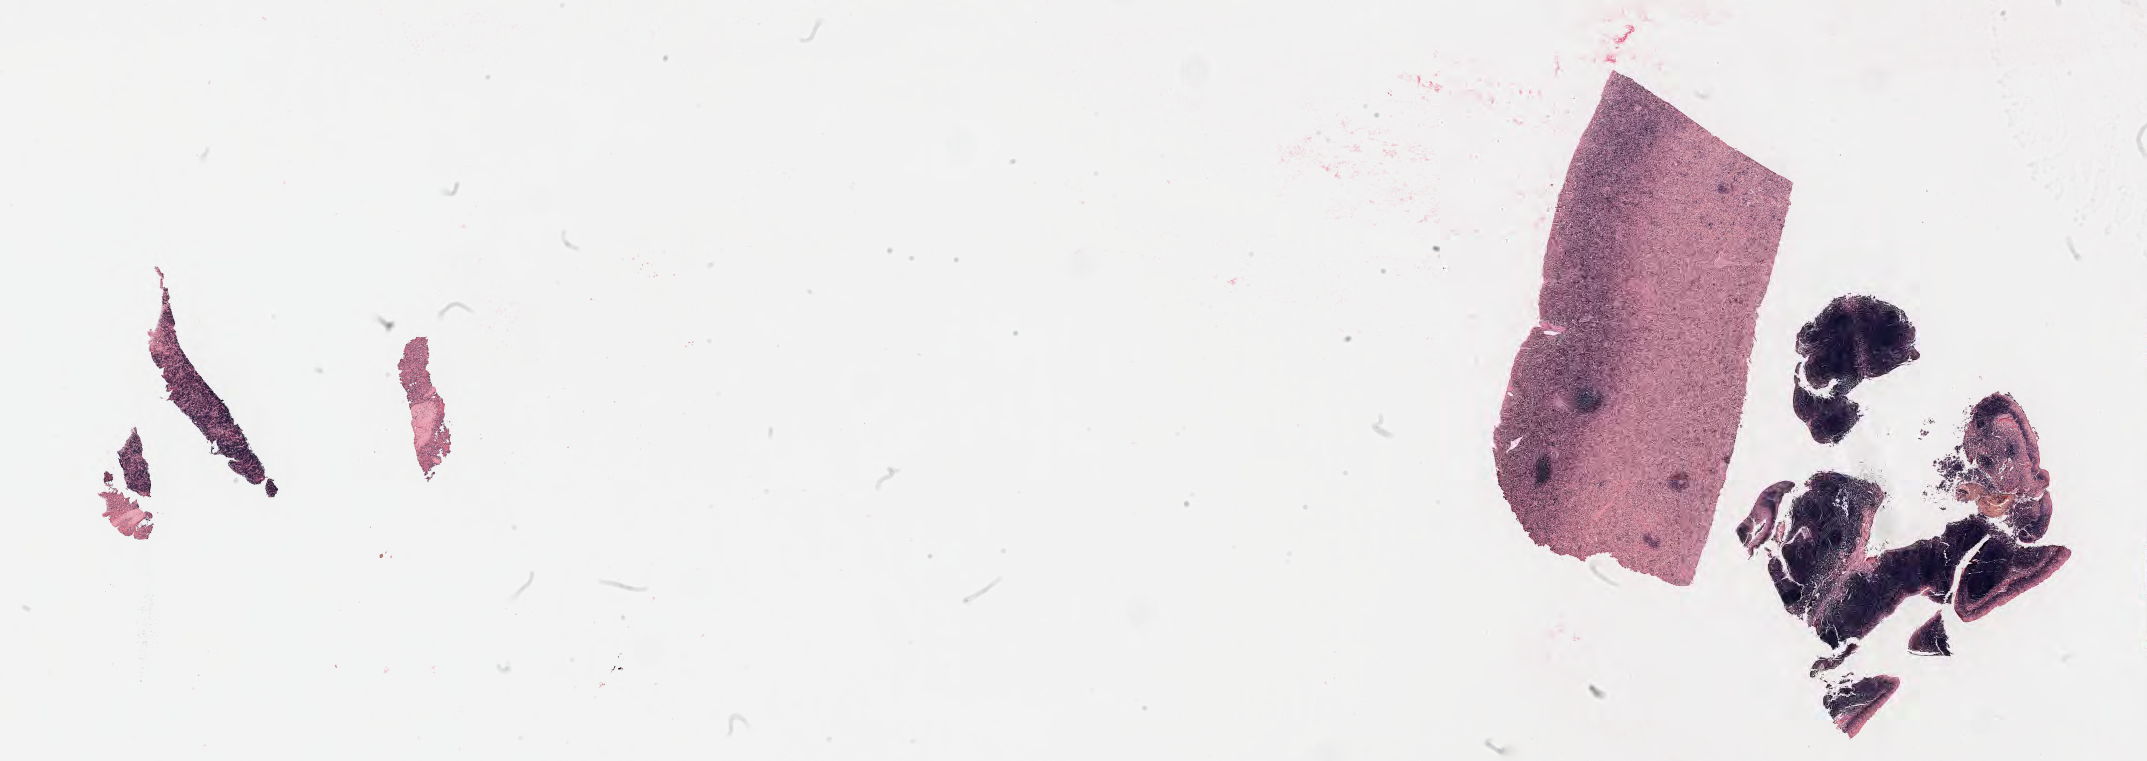
Whole-slide image; stain recorded as Iodonitrotetrazolium, a low-resolution overview of the entire scanned area, about 34.7 x 12.3 mm; tumor tissue. Male patient, age 13 years.
Histologic diagnosis: Diffuse large B-cell lymphoma, NOS.